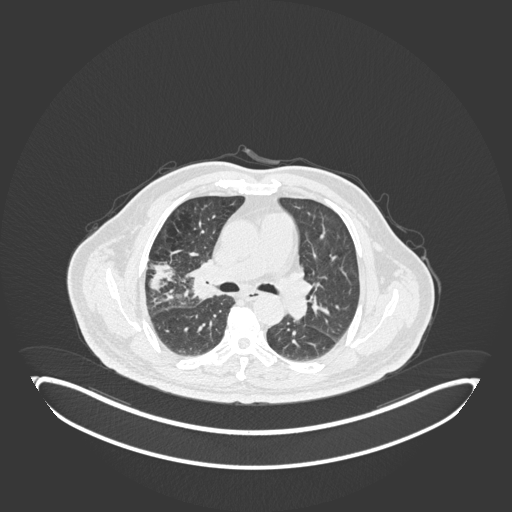
Chest CT, one axial slice; position 103 of 247 along the scan axis; reconstruction kernel B30f; lung window (W 1500 / L -600 HU); 1 mm slice thickness; 512 × 512 image matrix, field of view 500 × 500 mm. Patient: male, 72 years. Case-level facts recorded for this patient, not image findings: clinical TNM (as recorded): T1c N0 M0; histopathological grade: G2.
Outlined on this slice (rectangle marked by the reading radiologist):
- lung tumour (recorded histology: squamous cell carcinoma): bounding box <183,253,217,305> (left, top, right, bottom; pixels)